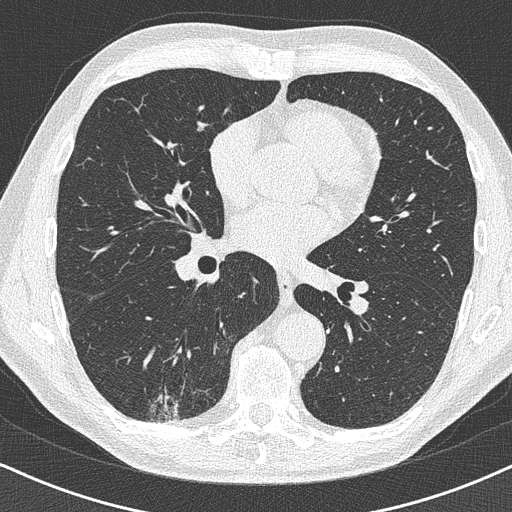
Axial slice from a low-dose chest CT screening exam, baseline annual screen, lung window (W 1500 / L -600 HU), 1 mm slice thickness, lung (sharp) reconstruction kernel (B50f), slice 224 of 438 in the series. Male participant, aged 63 years at enrolment. Former smoker at enrolment.
- Lesion marked by an expert reader, box from (x=129, y=359) to (x=201, y=427) px.
- The exam's reader record, not a measurement of the box and not confirmed to be the same lesion: non-calcified nodule or mass ≥4 mm, right lower lobe, 16 × 13 mm, poorly defined margins.
- Official screen result: positive, change unspecified: nodule(s) >= 4 mm or enlarging nodule(s), mass(es), or other non-specific abnormalities suspicious for lung cancer.